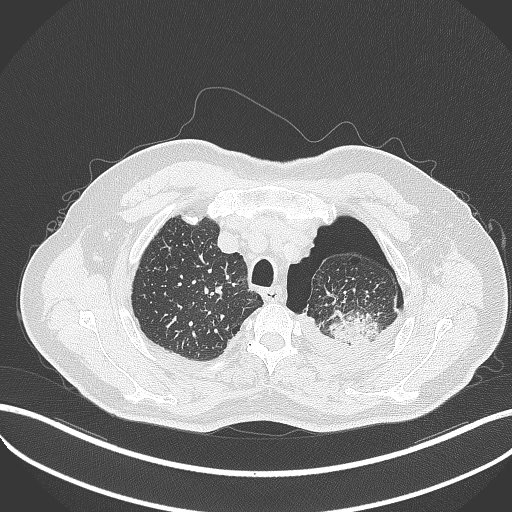
Chest CT, one axial slice. Position 416 of 464 along the scan axis. Lung window (W 1500 / L -600 HU). 512 × 512 image matrix, field of view 400 × 400 mm. Patient: male, 76 years. From the clinical record (not read from this slice): clinical TNM (as recorded): T3 N0 M1b.
Structures marked on this image (bounding box drawn by a radiologist):
- lung tumour (recorded histology: adenocarcinoma): bounding box <324,310,379,346> (left, top, right, bottom; pixels)